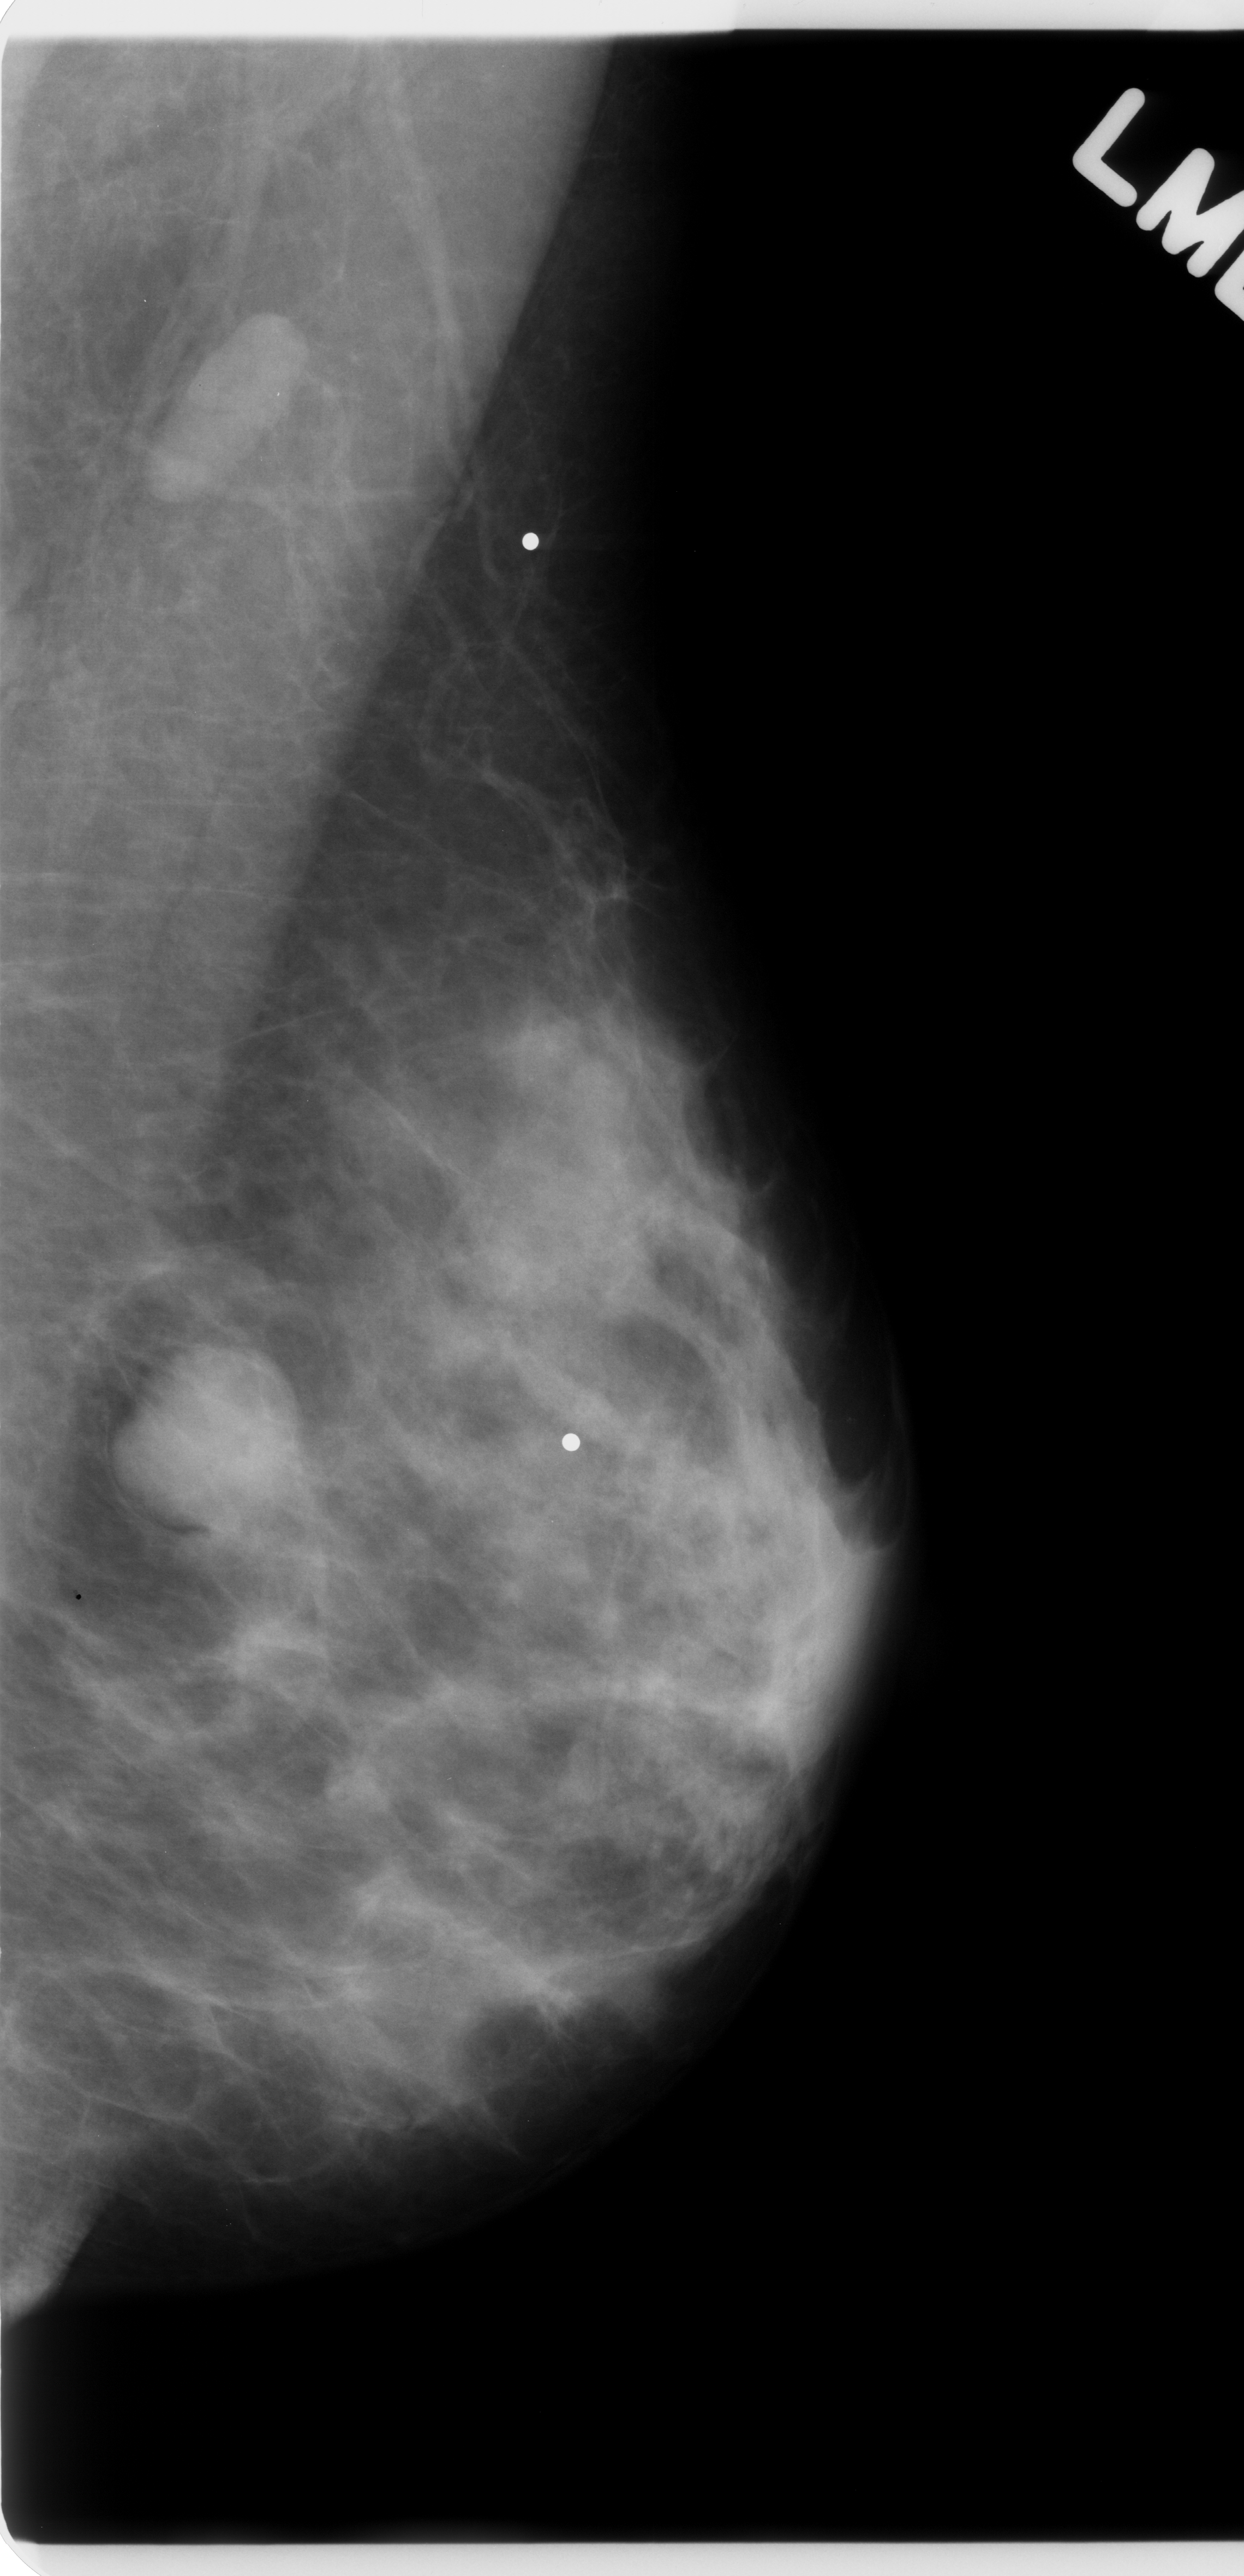
Digitized screen-film mammogram; left breast; mediolateral oblique (MLO) view; BI-RADS breast density category 2 (scale 1–4); 1244 × 2576 image matrix.
Marked abnormalities (boxes around the expert regions of interest):
- Finding 1 of 2: mass, shape round, margins circumscribed; BI-RADS assessment category 4; subtlety rating 5 on a 1 (subtle) to 5 (obvious) scale; pathology result (as recorded, not read from the image): malignant: bounding box <111,1337,311,1531> (left, top, right, bottom; pixels)
- Finding 2 of 2: mass, shape oval, margins circumscribed; BI-RADS assessment category 5; pathology result (as recorded, not read from the image): malignant: <144,315,308,501>